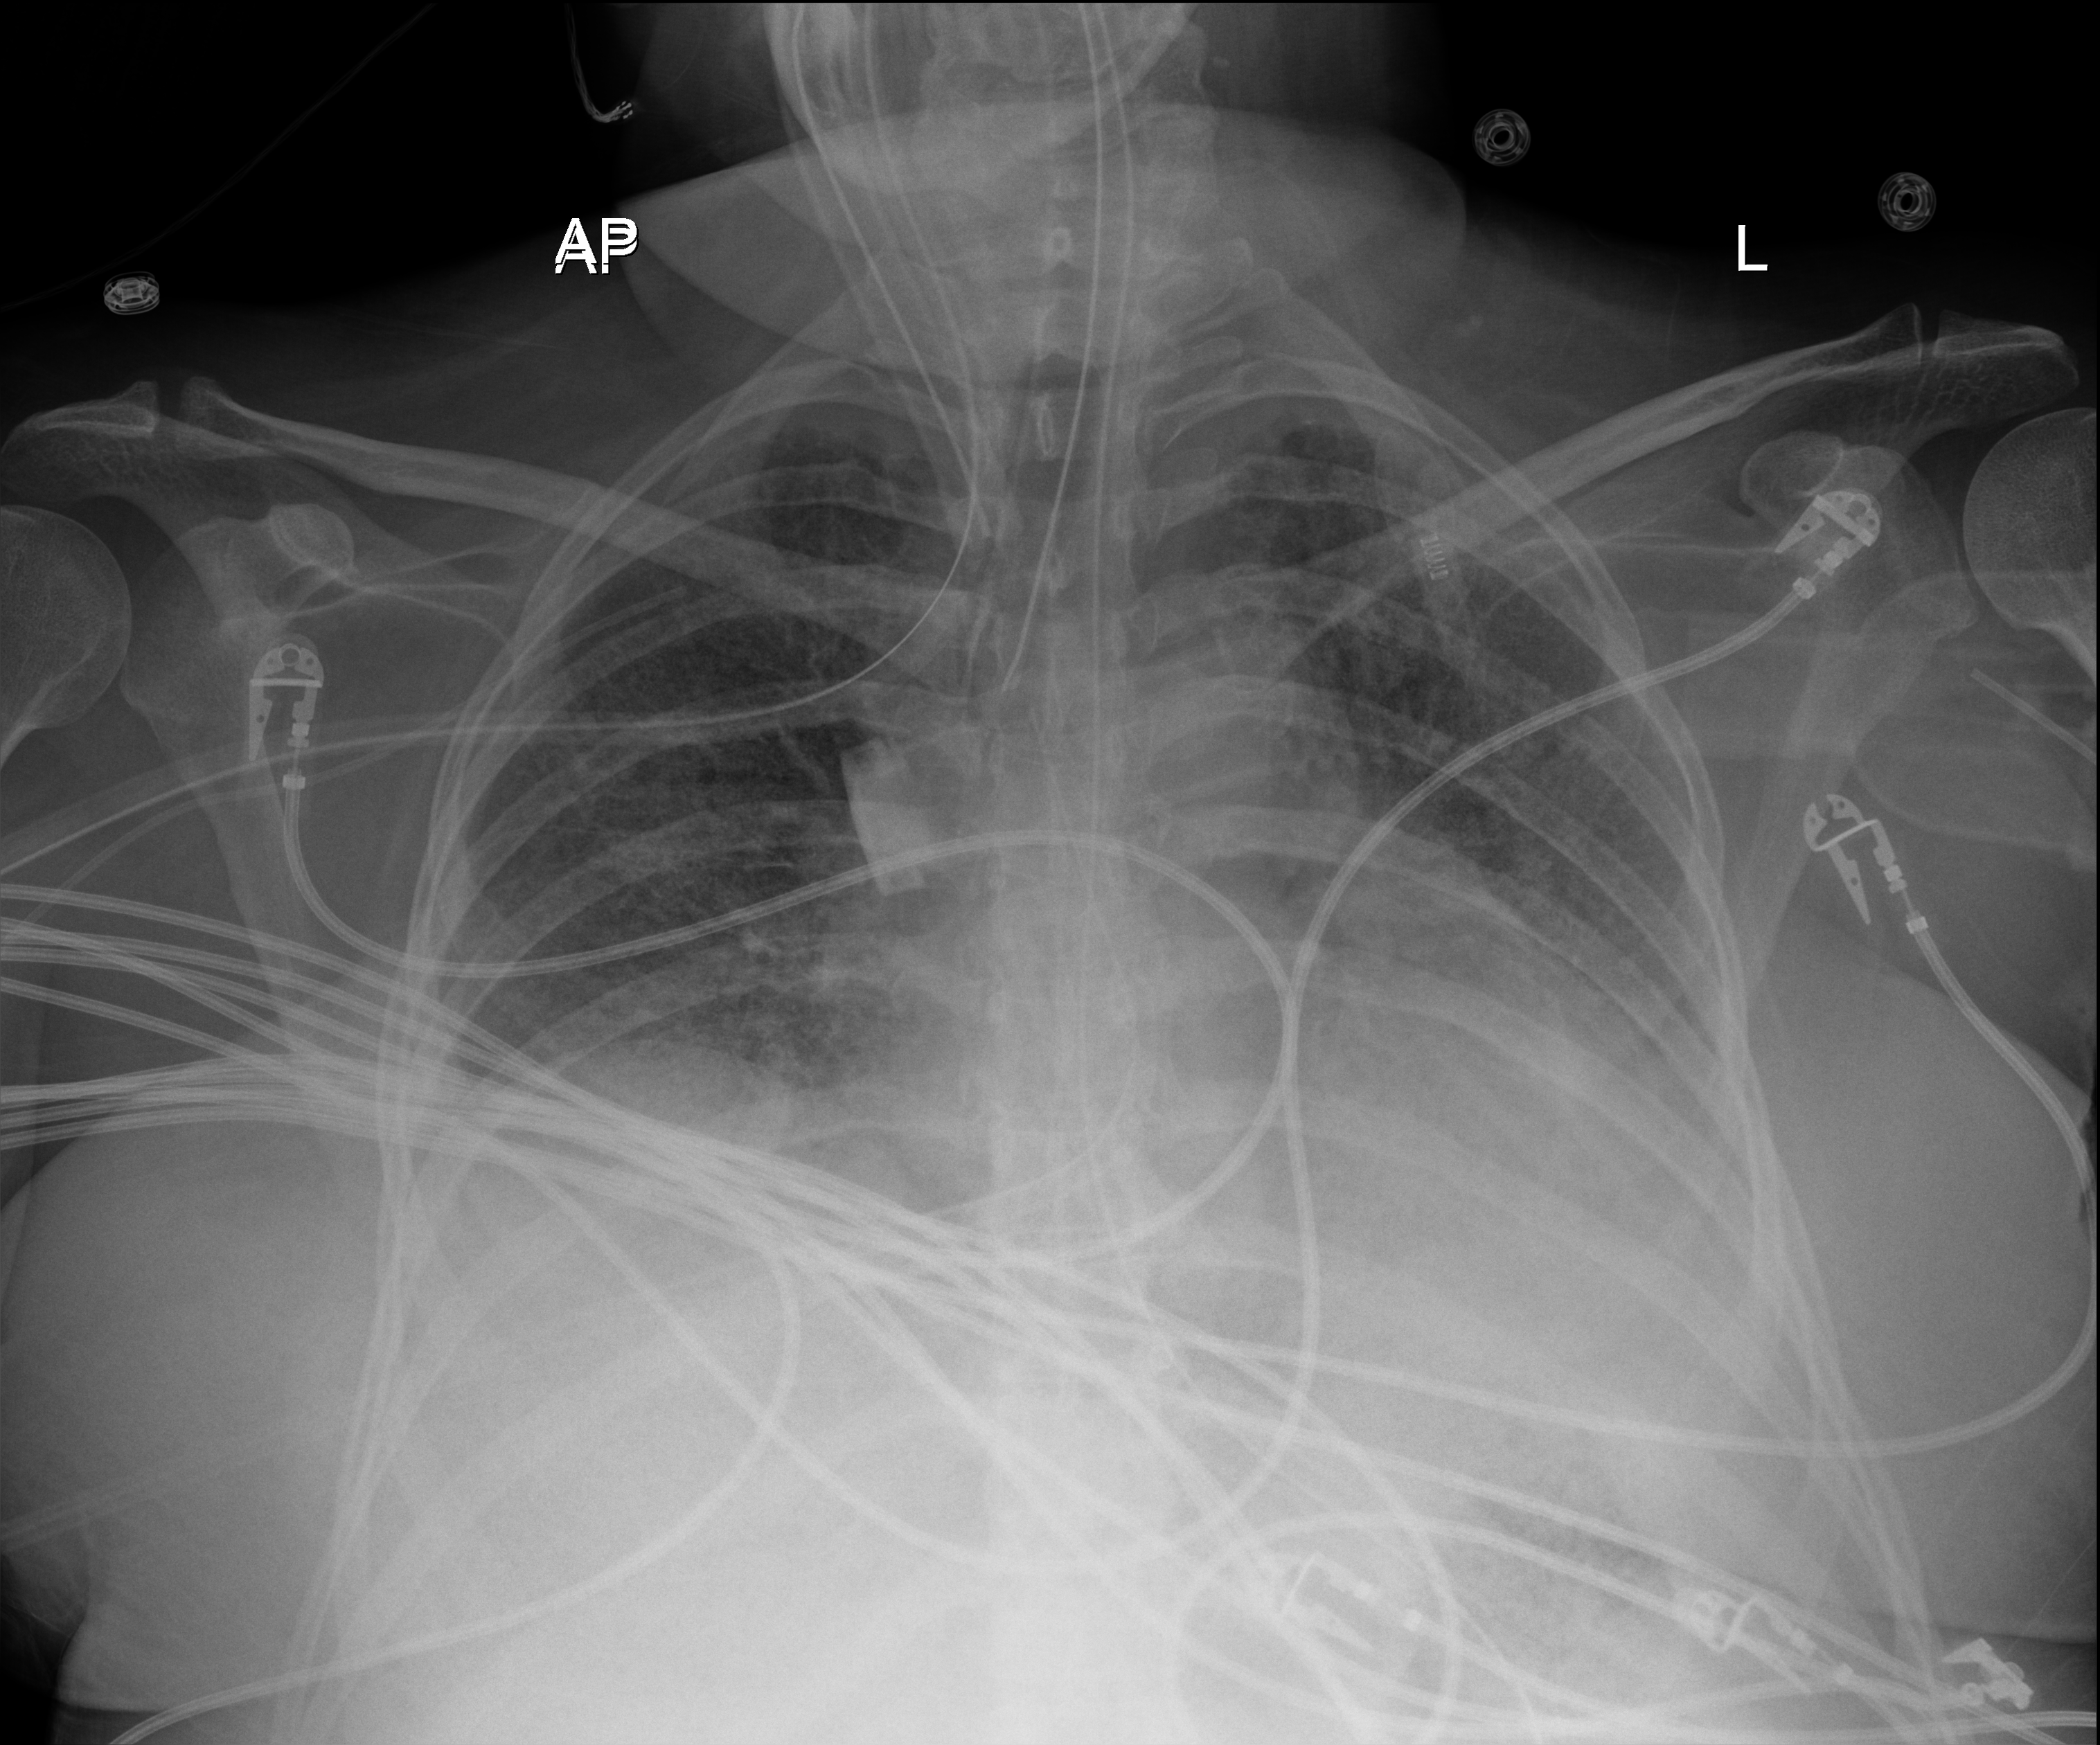
Portable chest radiograph; anteroposterior (AP) projection. Female patient hospitalised with COVID-19, age 18–59 years.
Admission-level facts for this patient (not findings on this image; timing relative to this image not recorded): chronic kidney disease (admission record): no; admitted to intensive care during this hospital stay: yes; length of hospital stay: 73 days.